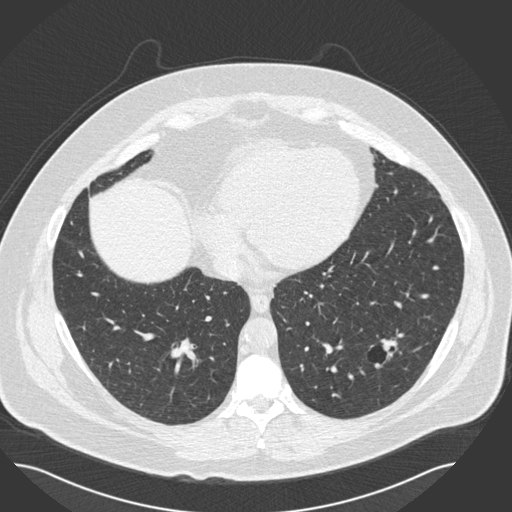
Low-dose screening chest CT, axial slice, second annual screen, lung window (W 1500 / L -600 HU), 2 mm slice thickness. Male, age 57 years at enrolment. Current smoker at enrolment.
• Lesion marked by an expert reader, bounding box [x1, y1, x2, y2] px = [356, 324, 422, 381].
• Screening reader's record for this exam (one nodule recorded; not confirmed to be the boxed lesion): non-calcified nodule or mass ≥4 mm, left lower lobe, 19 × 15 mm, pre-existing on the prior screen: yes; interval growth: no.
• Official screen result: positive, no significant change: stable abnormalities potentially related to lung cancer, unchanged since the prior screening exam.
• Participant outcome: lung cancer diagnosed 434 days after this screen — squamous cell carcinoma, NOS, left lower lobe, moderately differentiated (G2), stage IA (AJCC 6th edition), 22 mm at pathology.